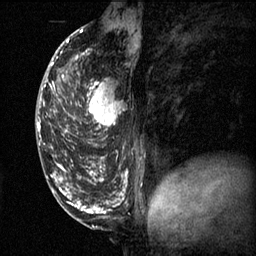
Breast MRI (dynamic contrast-enhanced), one sagittal slice. 3 images stored at this slice position (order not interpretable as contrast timing). 1.5 T. TE 4.2 ms, TR 11.1 ms. 256 × 256 image matrix, field of view 180 × 180 mm. Female patient, age 50 years.
Annotated regions visible in this slice (semi-automatically segmented with operator editing):
- analysis volume of interest (the breast-tissue region the enhancement analysis was run in; not a lesion): box from (x=68, y=68) to (x=130, y=141) px
- tumour enhancement mask (voxels above the 70 % enhancement threshold inside the analysis volume of interest): (x=68, y=72)–(x=123, y=137)